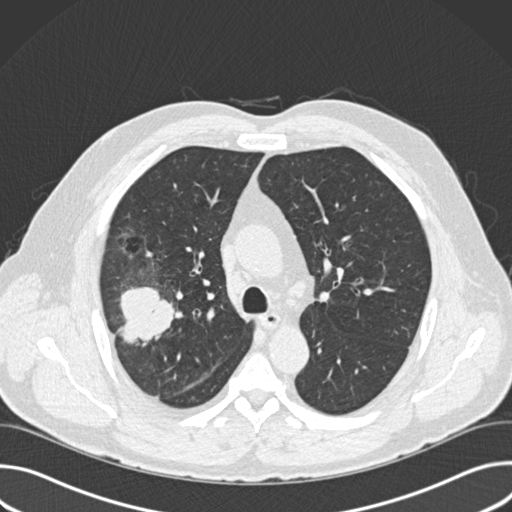
Low-dose screening chest CT, one axial slice. Slice 110 of 157 in the series (ordered by position). Reconstruction kernel B30f. 120 kVp. Lung window (W 1500 / L -600 HU). 2 mm slice thickness. 512 × 512 image matrix, field of view 380 × 380 mm.
Structures marked on this image (outlined manually by an expert reader):
- lesion 1 (tumor, upper lobe of right lung): bounding box (x1, y1, x2, y2) in pixels: (118, 287, 175, 344)